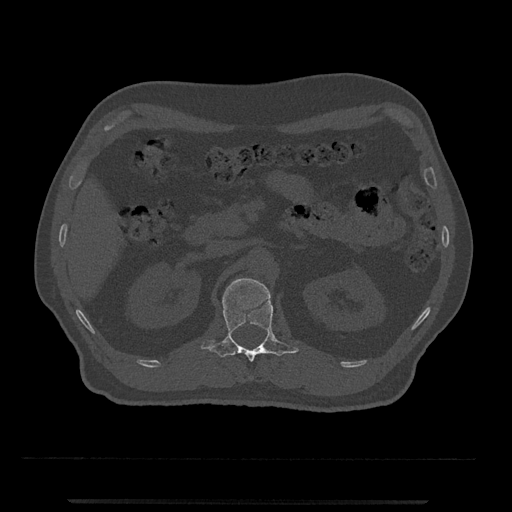
CT including the spine, one axial slice; position 339 of 797 along the scan axis; reconstruction kernel Br40s/3; 120 kVp; bone window (W 1800 / L 400 HU); 0.5 mm slice thickness; 512 × 512 image matrix. Male patient, age 63 years. From the clinical record (not read from this slice): primary cancer: prostate.
Annotated regions visible in this slice (semi-automatically segmented with operator editing):
- L1 vertebra: bounding box <201,278,299,362> (left, top, right, bottom; pixels)